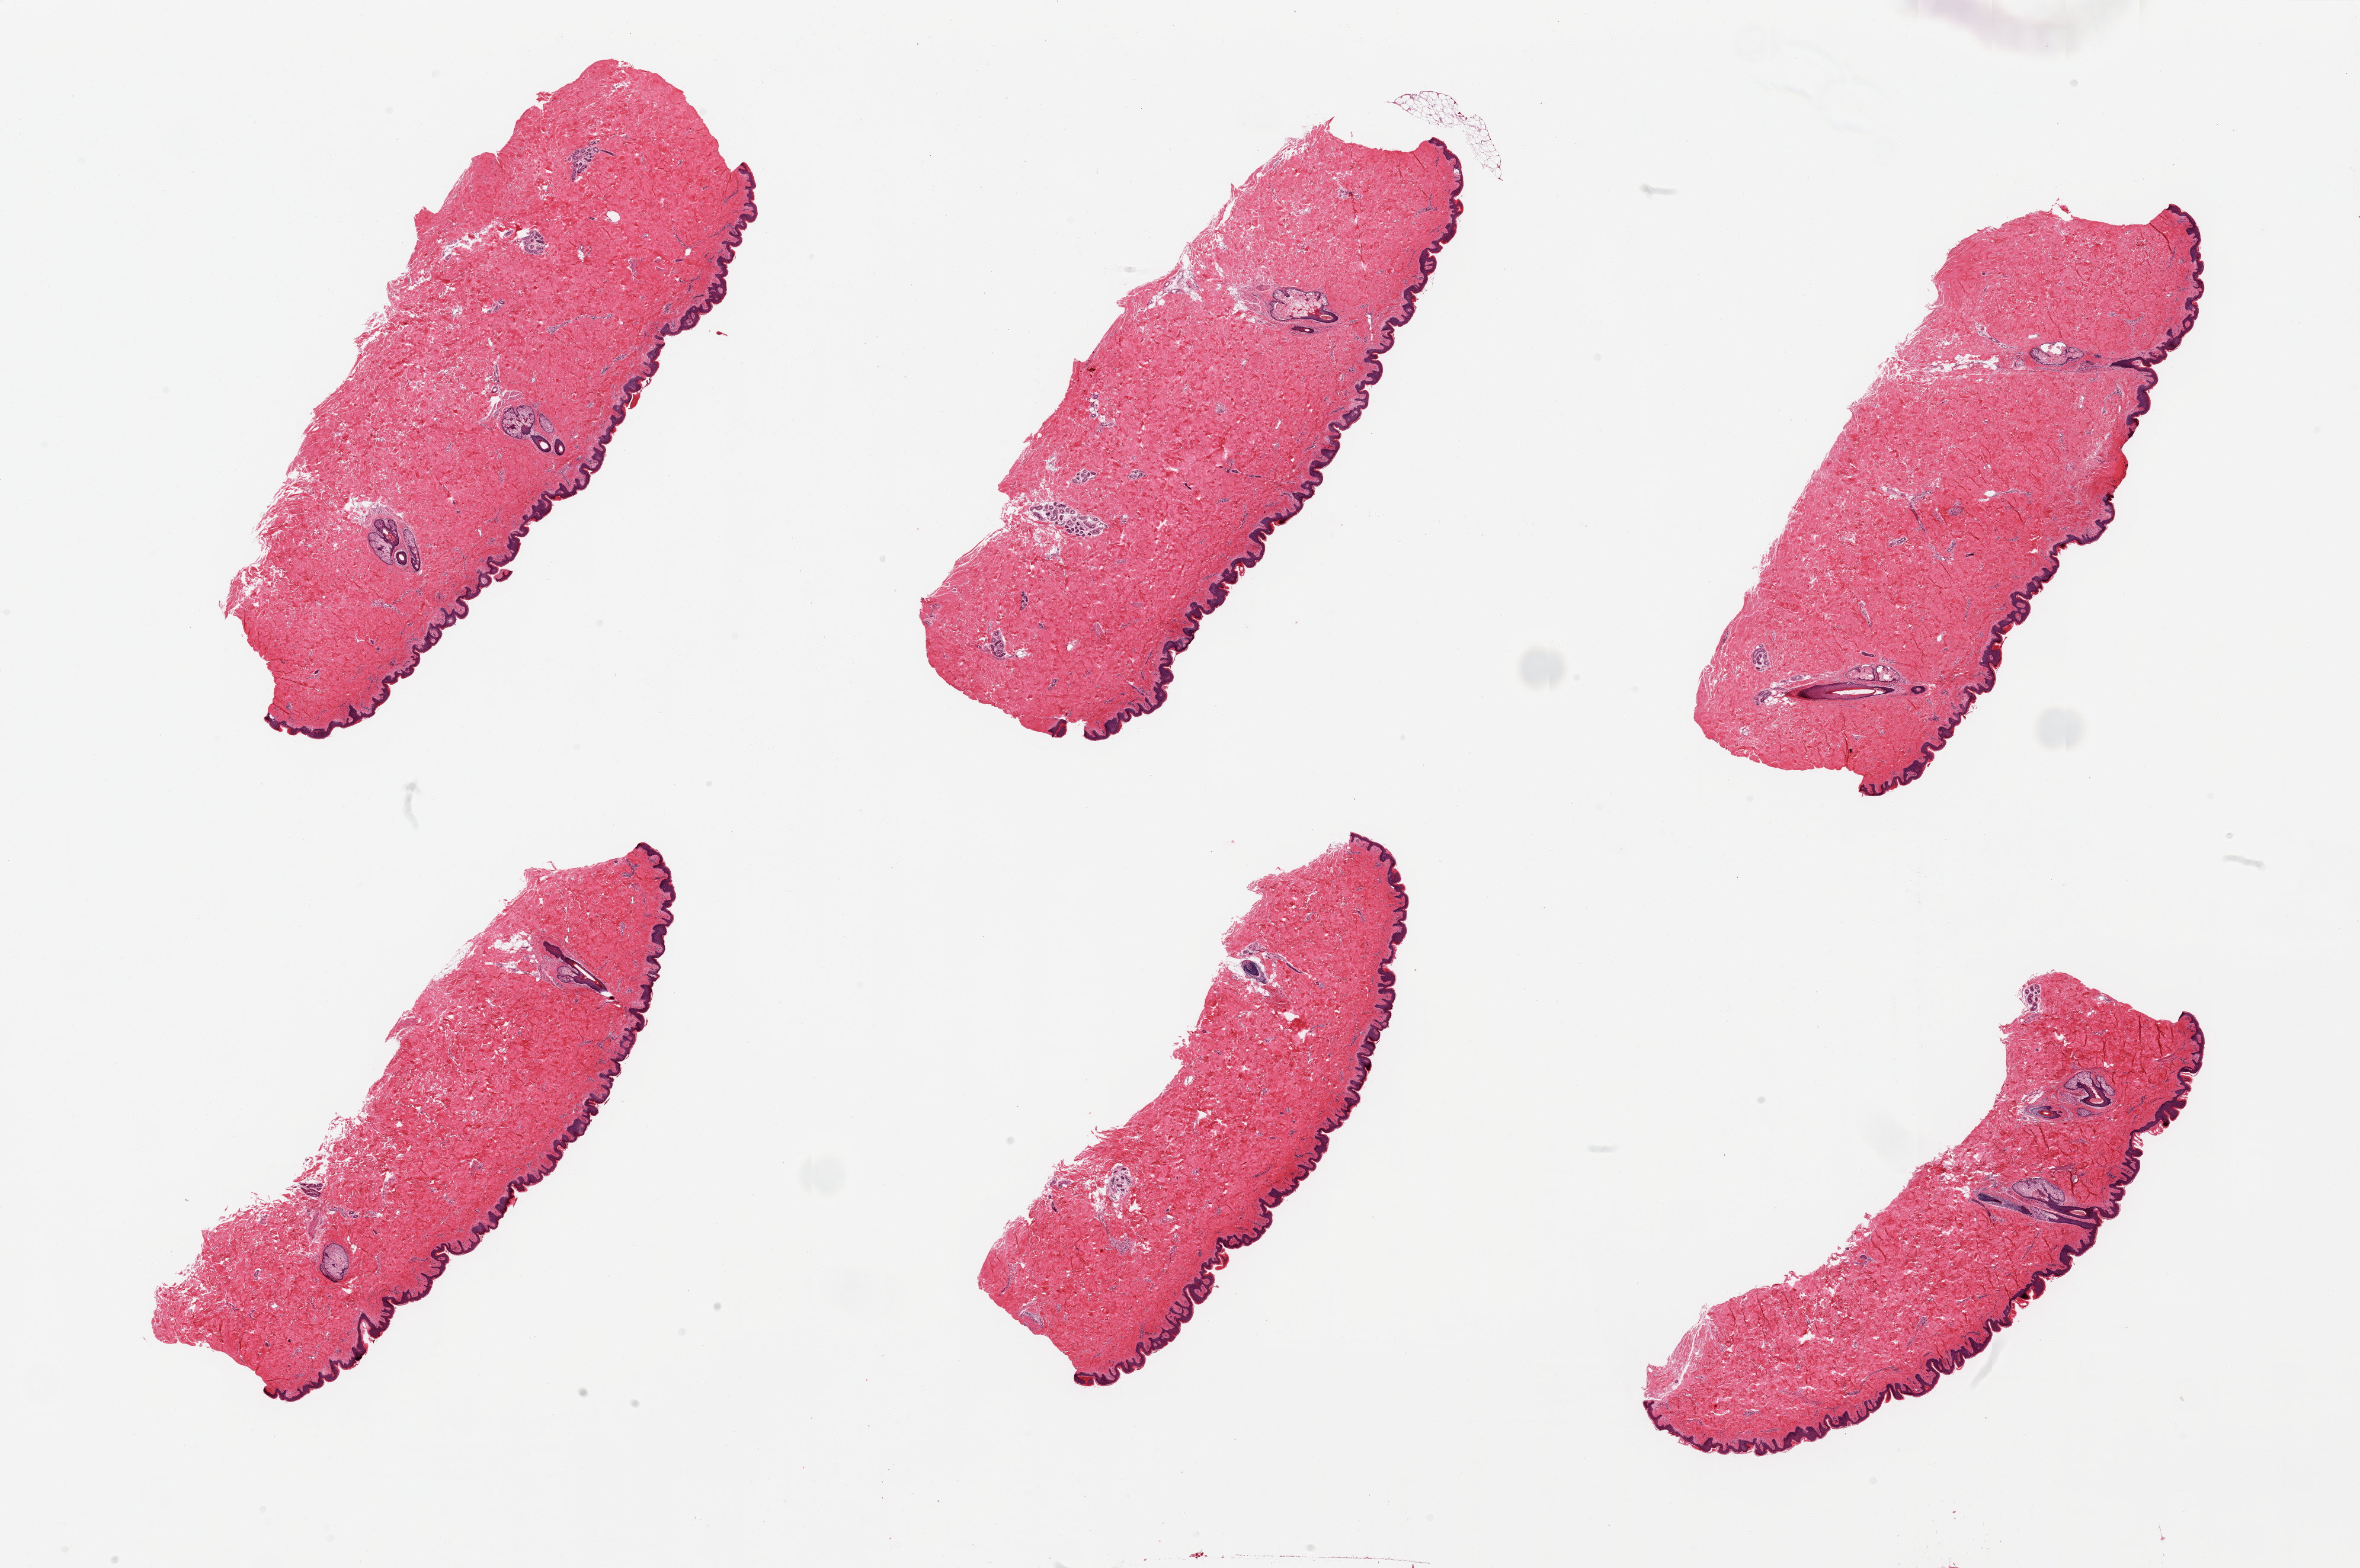
Digitized hematoxylin and eosin (H&E)-stained section, low-resolution overview of the scanned area, about 31.5 x 20.9 mm, PAXgene-fixed paraffin-embedded (PFPE) section, target tissue: skin of suprapubic region, tissue donor sample. Donor sex: male.
- review note (as recorded): 6 pieces; well trimmed